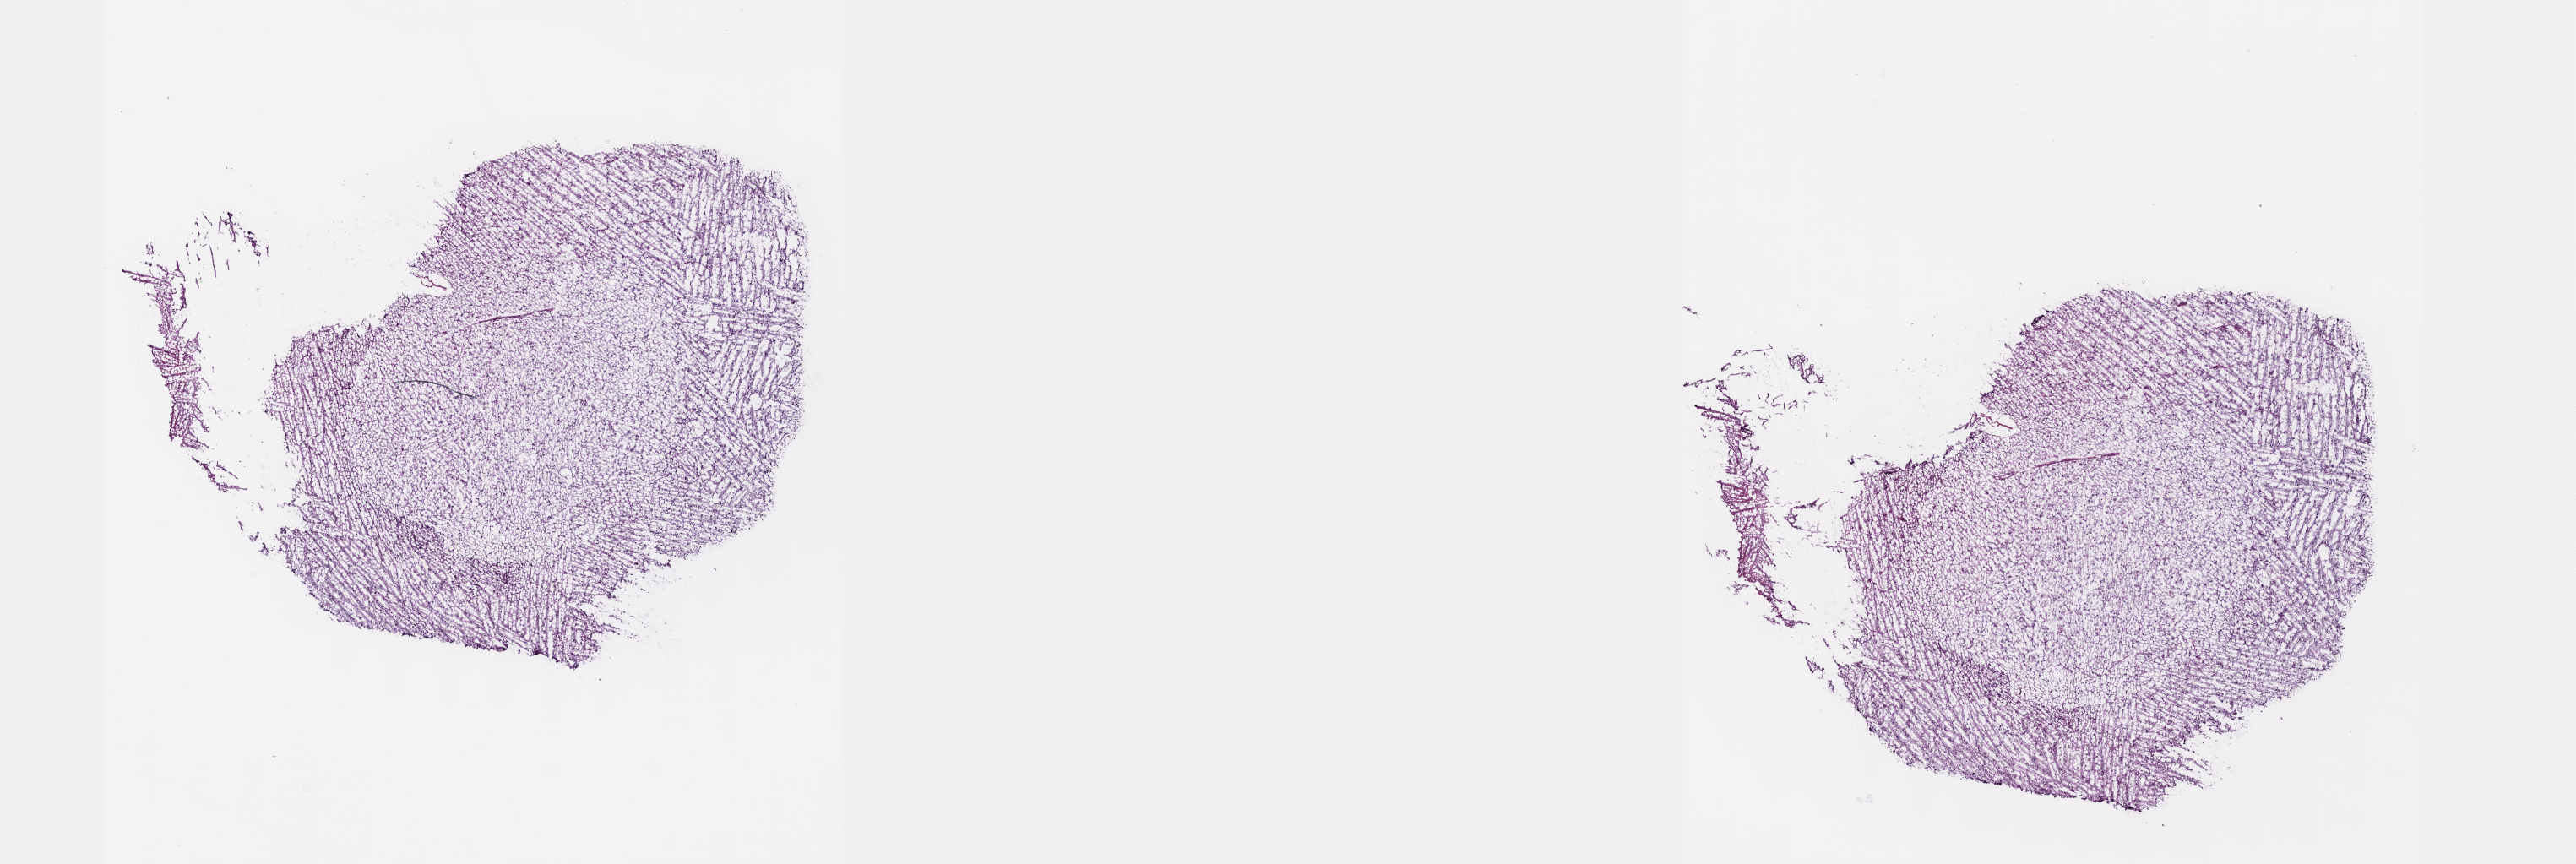
Whole-slide histology image, H&E-stained — whole scanned area (about 24.6 x 8.3 mm) shown as a low-resolution overview; frozen section from the top of the tissue portion; brain, primary tumour sample. Patient: male, age at initial diagnosis 28 years. Histologic grade: G2 (moderately differentiated). Slide review estimates, as recorded: tumour cells 30%, tumour nuclei 80%, normal cells 10%, stromal cells 60%, necrosis 0%. Infiltration values recorded for this section: lymphocyte infiltration 0%, monocyte infiltration 0%, neutrophil infiltration 0%.
Histologic diagnosis: Mixed glioma (cerebrum).